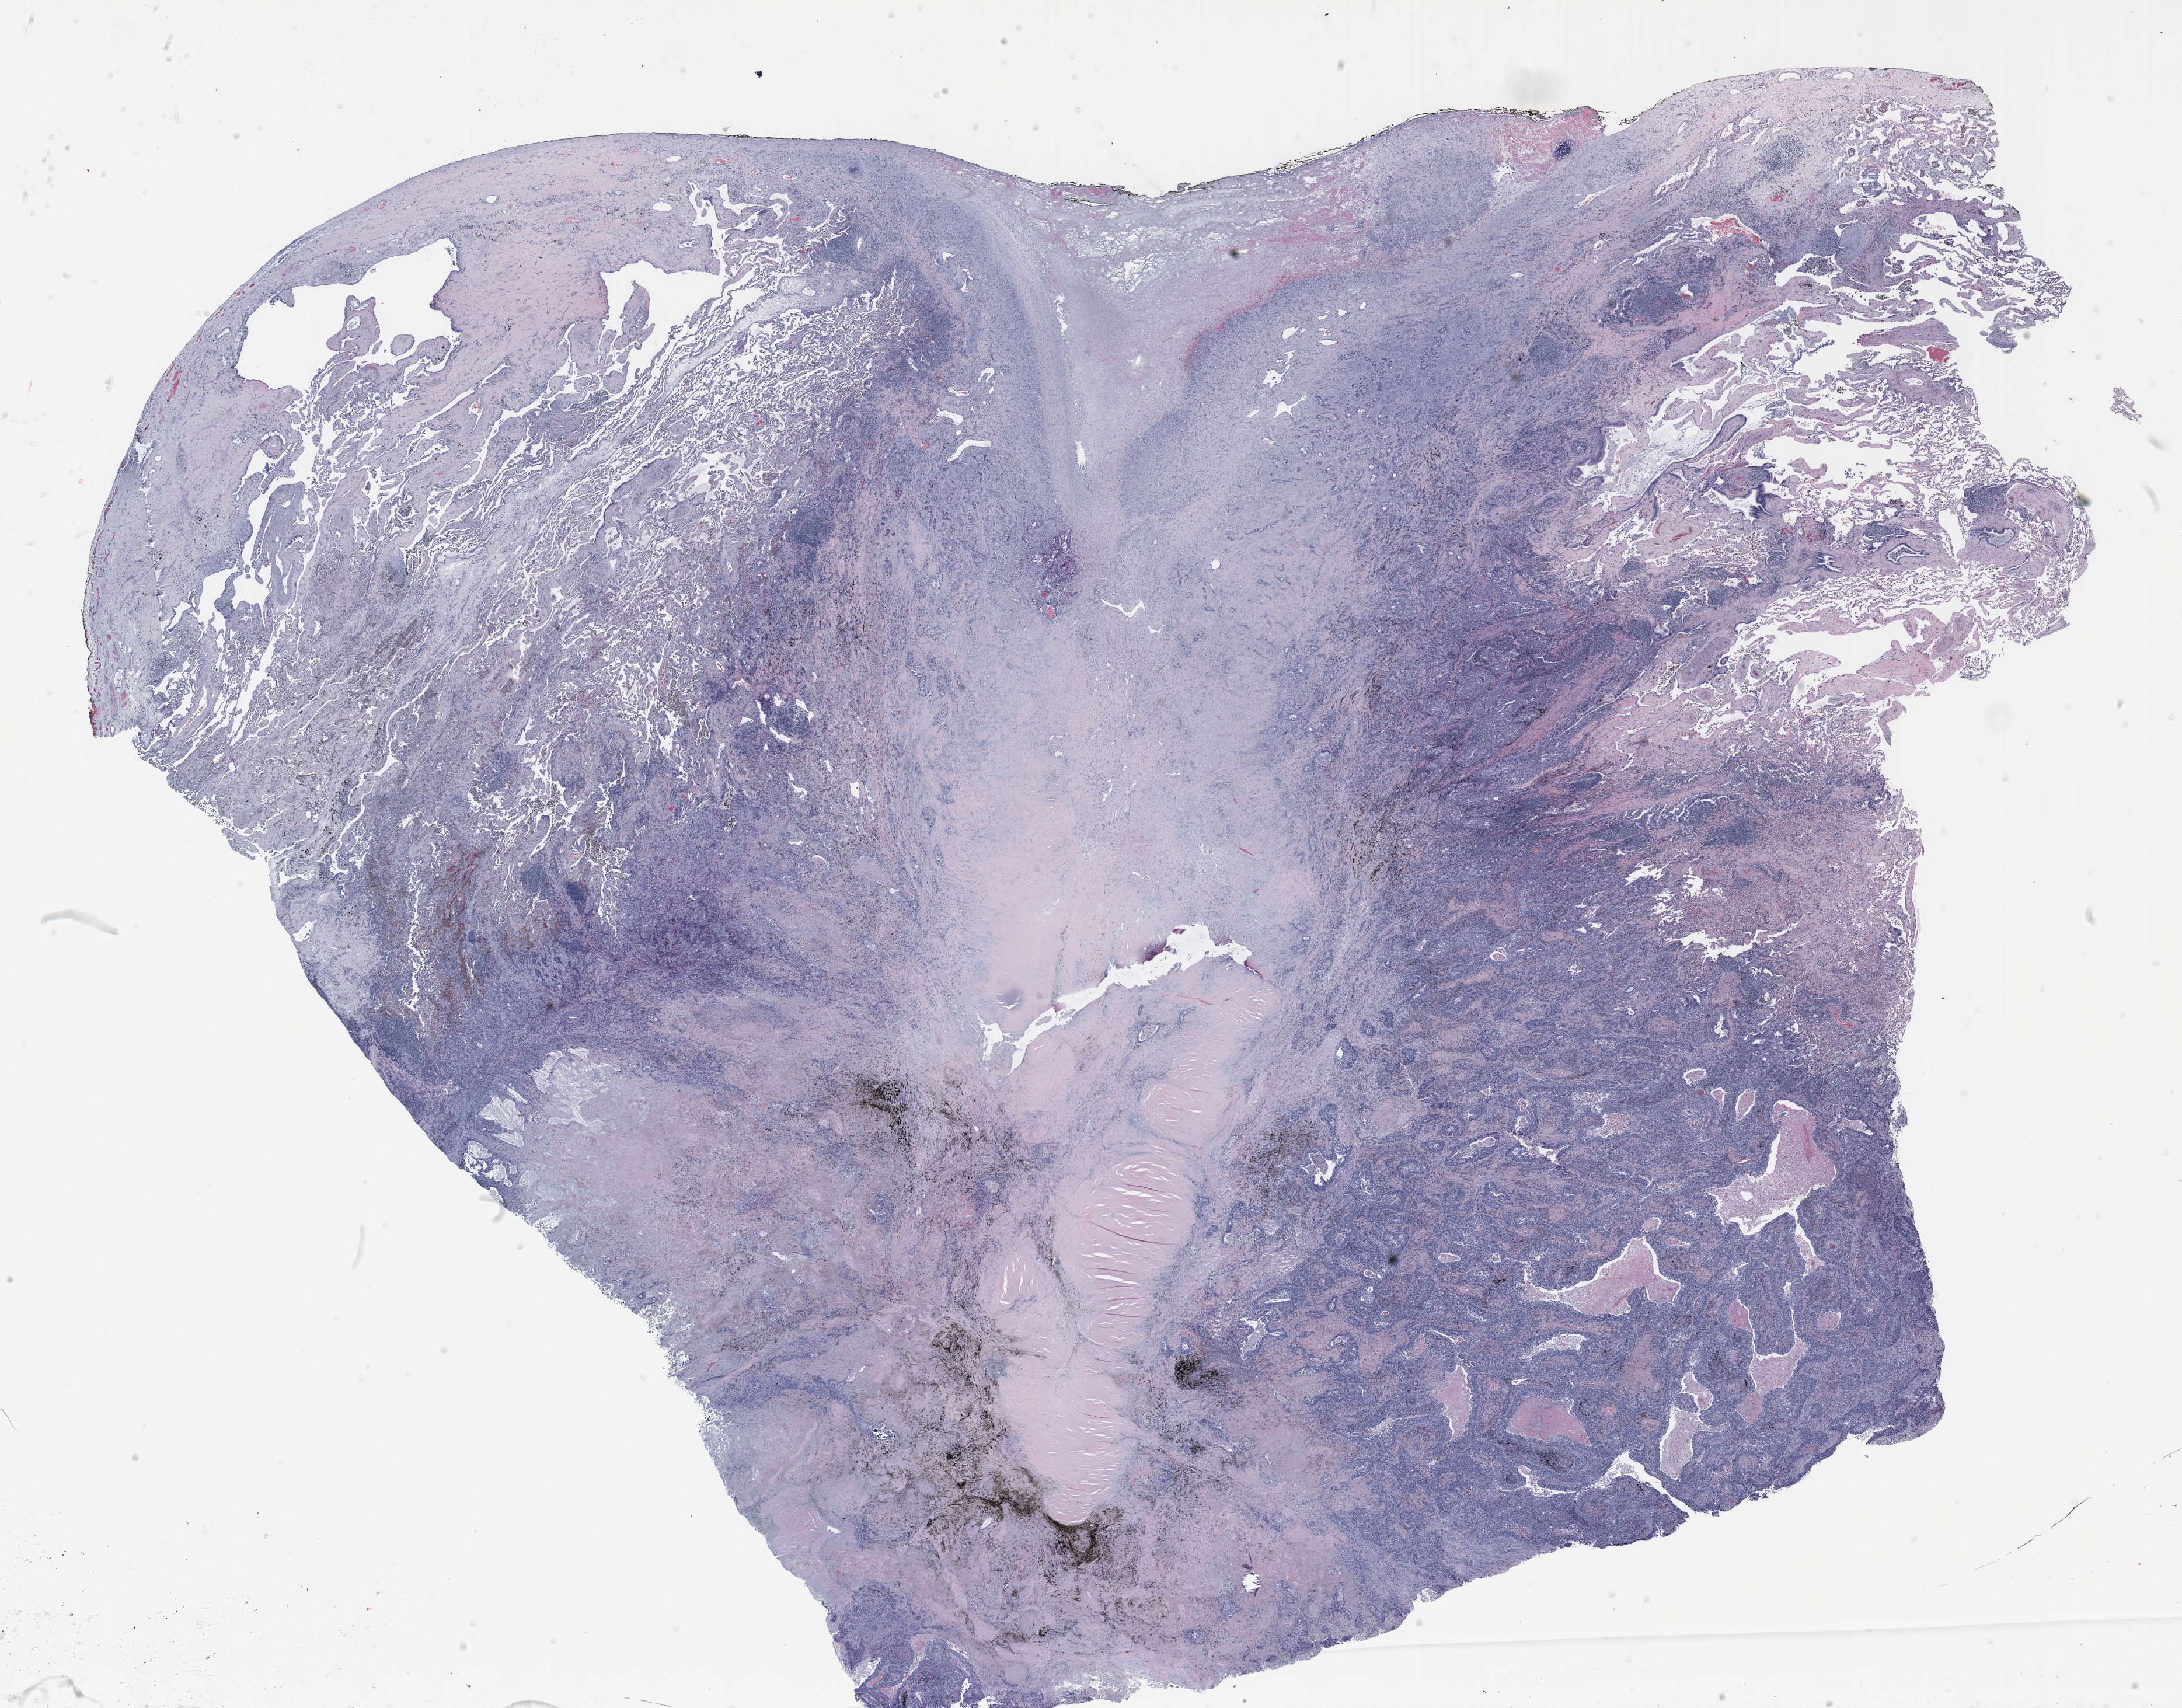
H&E whole-slide image — shown as a low-resolution overview of the whole scanned area (about 30.0 x 23.5 mm), formalin-fixed paraffin-embedded (FFPE) section, lung tissue. Male, age 71 at enrolment. Current smoker at enrolment. Grade: poorly differentiated (G3).
ICD-O-3 topography: upper lobe of lung (C34.1). Tumour size (pathology): 30 mm. Stage (AJCC 6th edition): IA. Primary tumour location (clinical record): right upper lobe. Participant's lung-cancer diagnosis: Squamous cell carcinoma, NOS (ICD-O-3 8070/3).